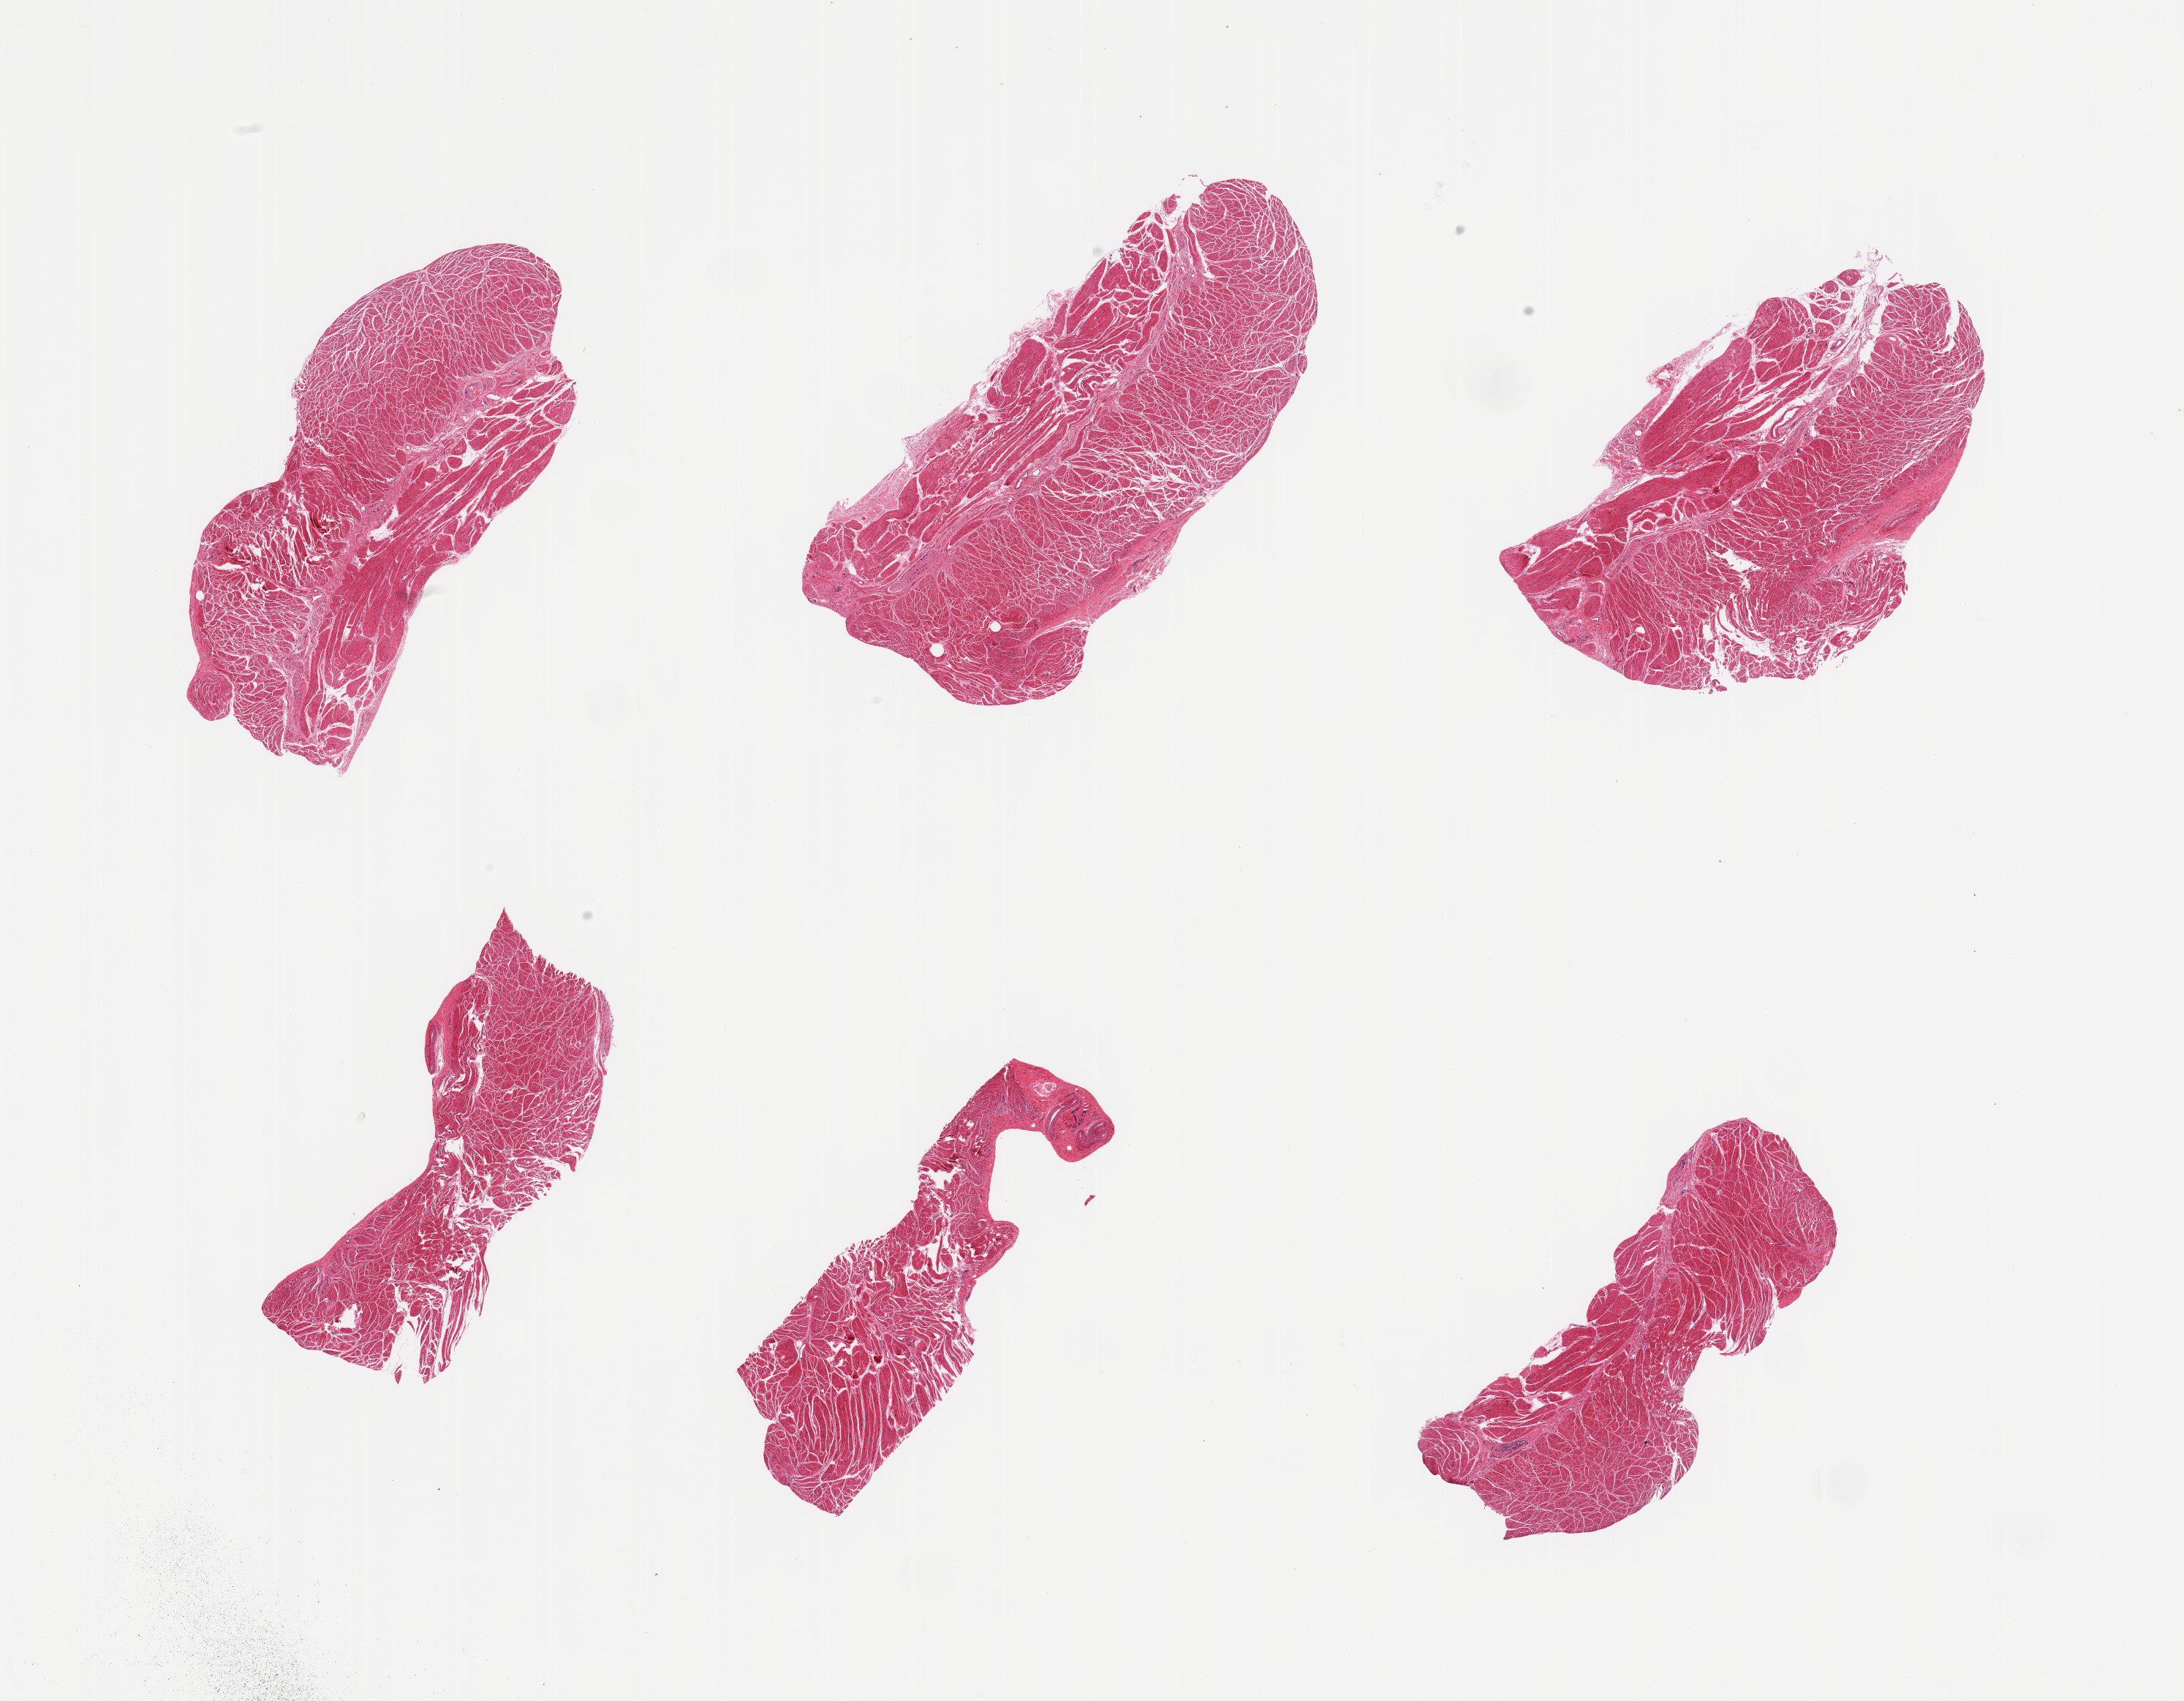
Whole-slide image, H&E stain — shown as a low-resolution overview of the whole scanned area (about 23.6 x 18.4 mm, acquisition: 20x scan); PAXgene-fixed, paraffin-embedded tissue; section of esophageal muscle (target tissue); donor tissue sample. Donor sex: female.
Review note (as recorded): 6 pieces, confirmed target muscularis.